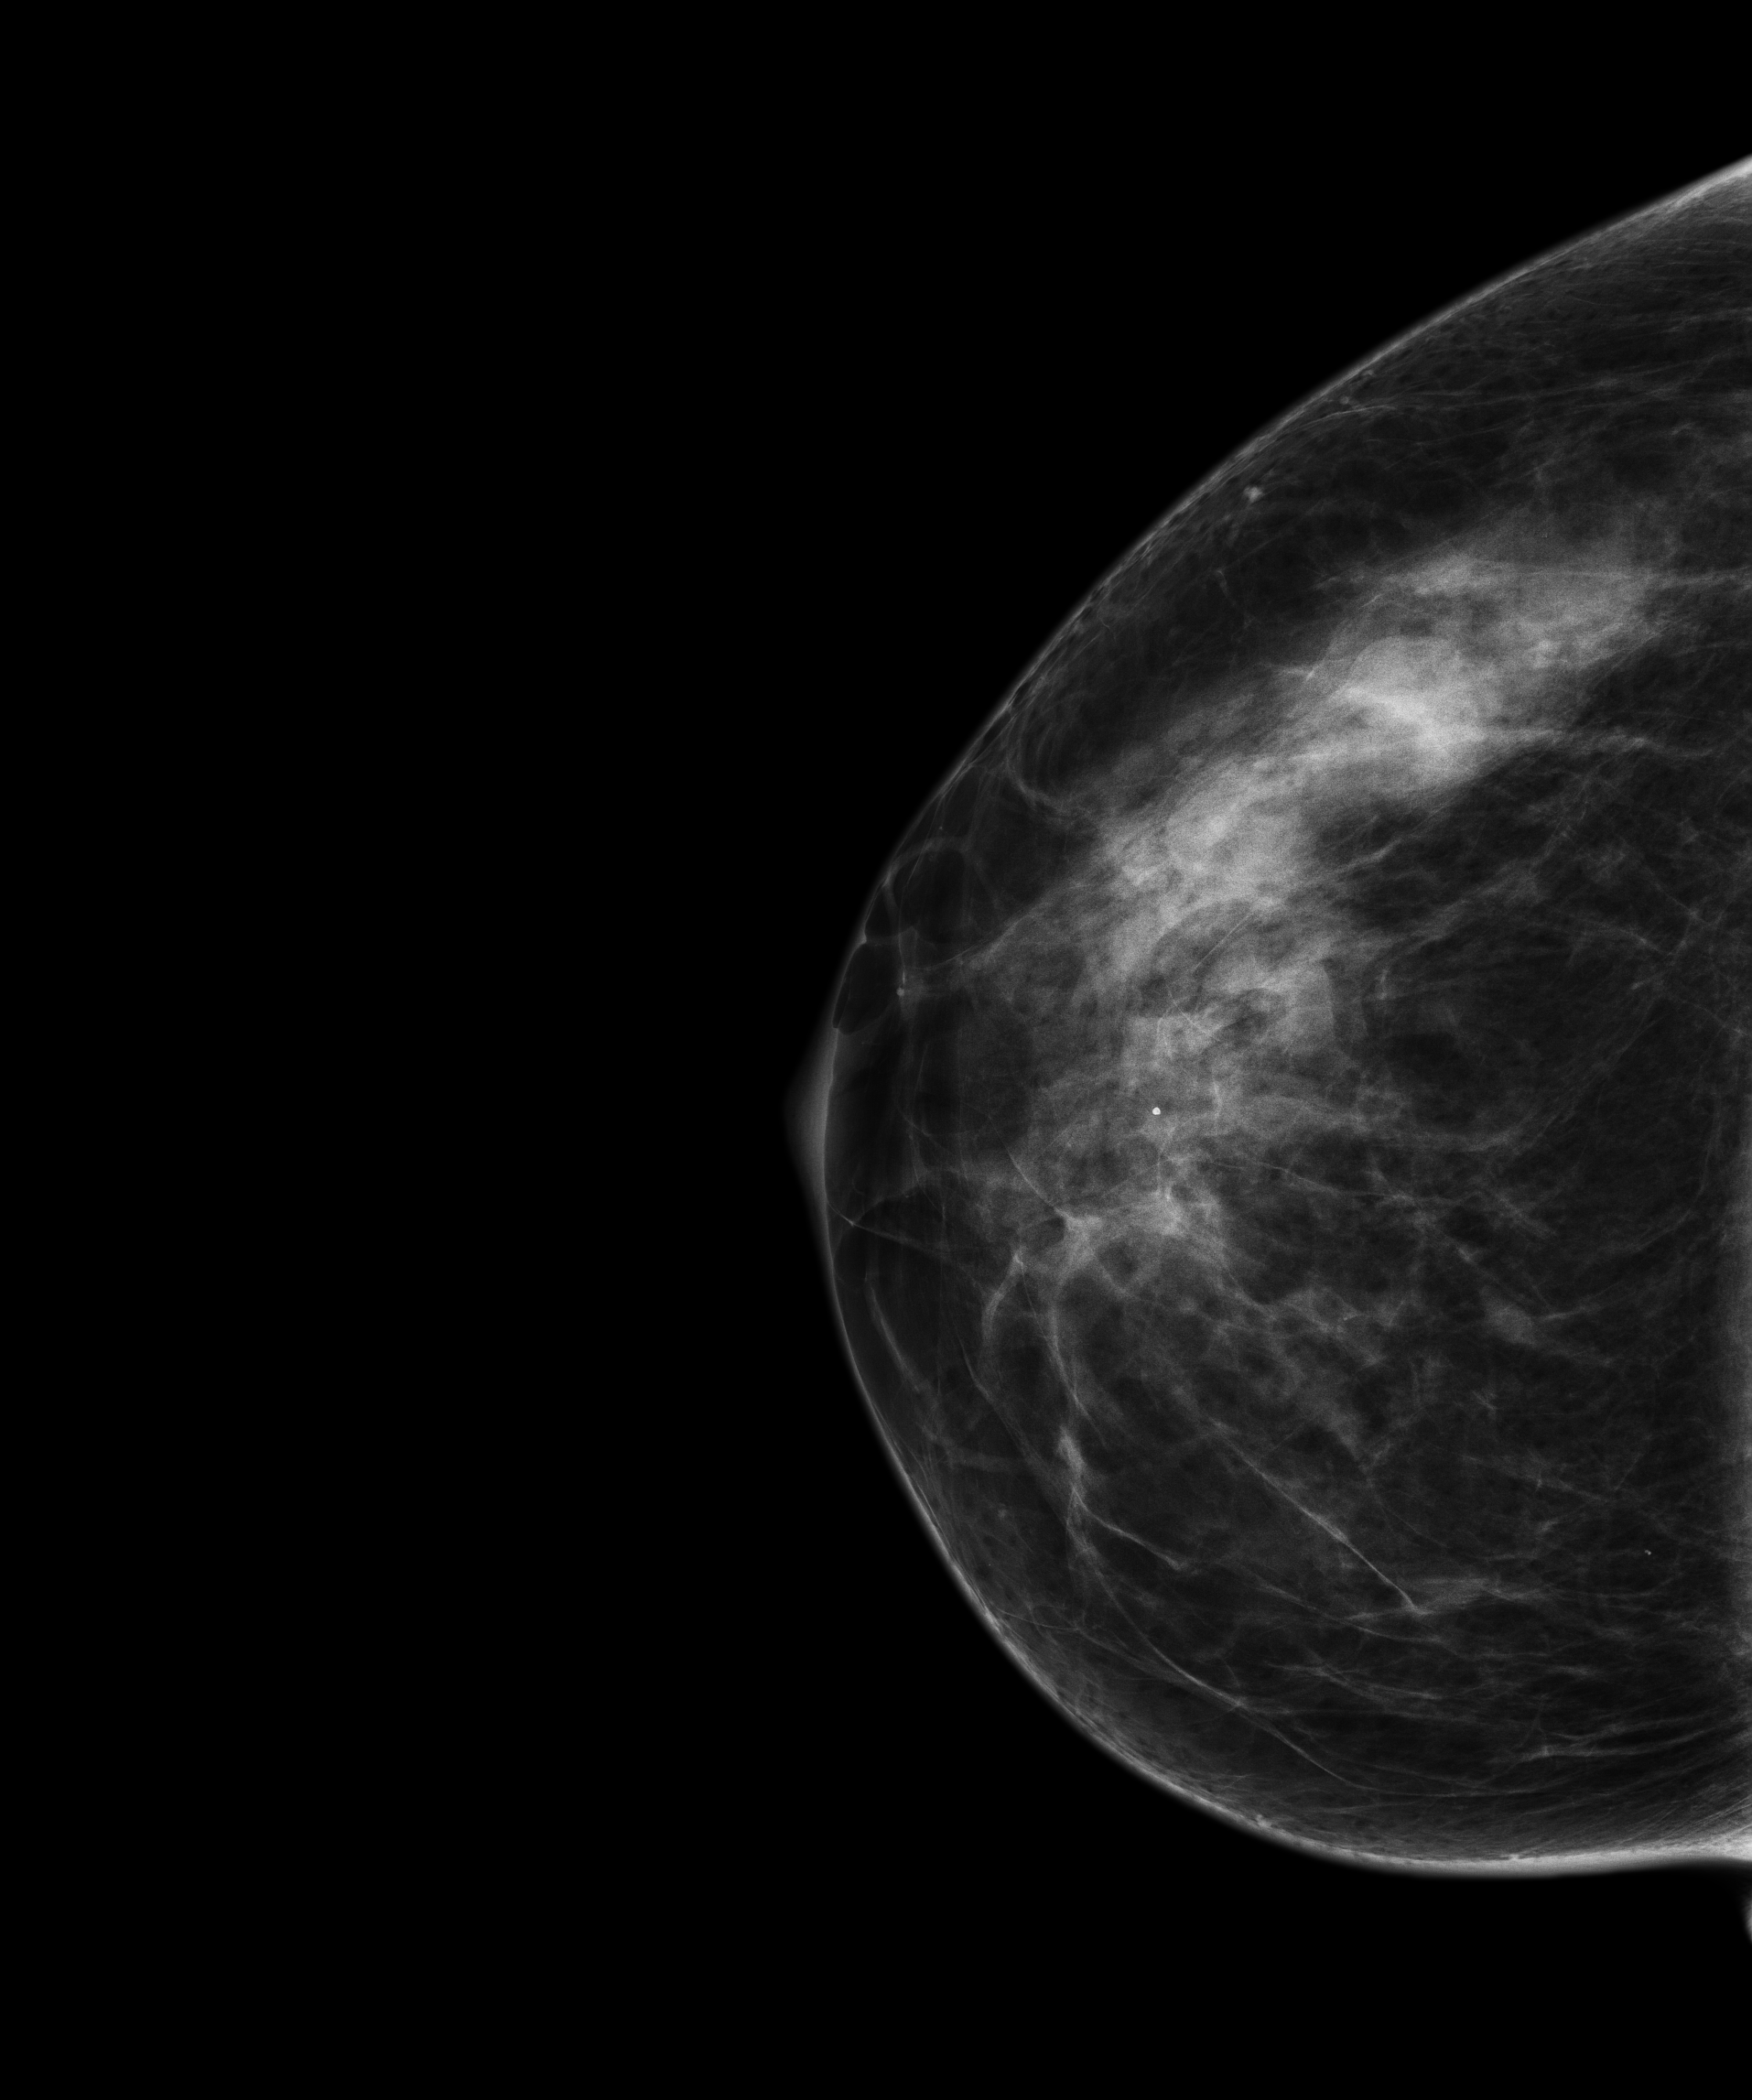
Full-field digital mammogram (FFDM), right breast, CC view, annual screening mammography examination, system: Senographe Essential ADS_56.21.3. Patient aged 51 years (female).
Breast density at the screening exam (both breasts): heterogeneously dense (BI-RADS density category c). Final BI-RADS category for the screening round (tomosynthesis exam, both breasts): category 2. Recall: no recall after this screen.